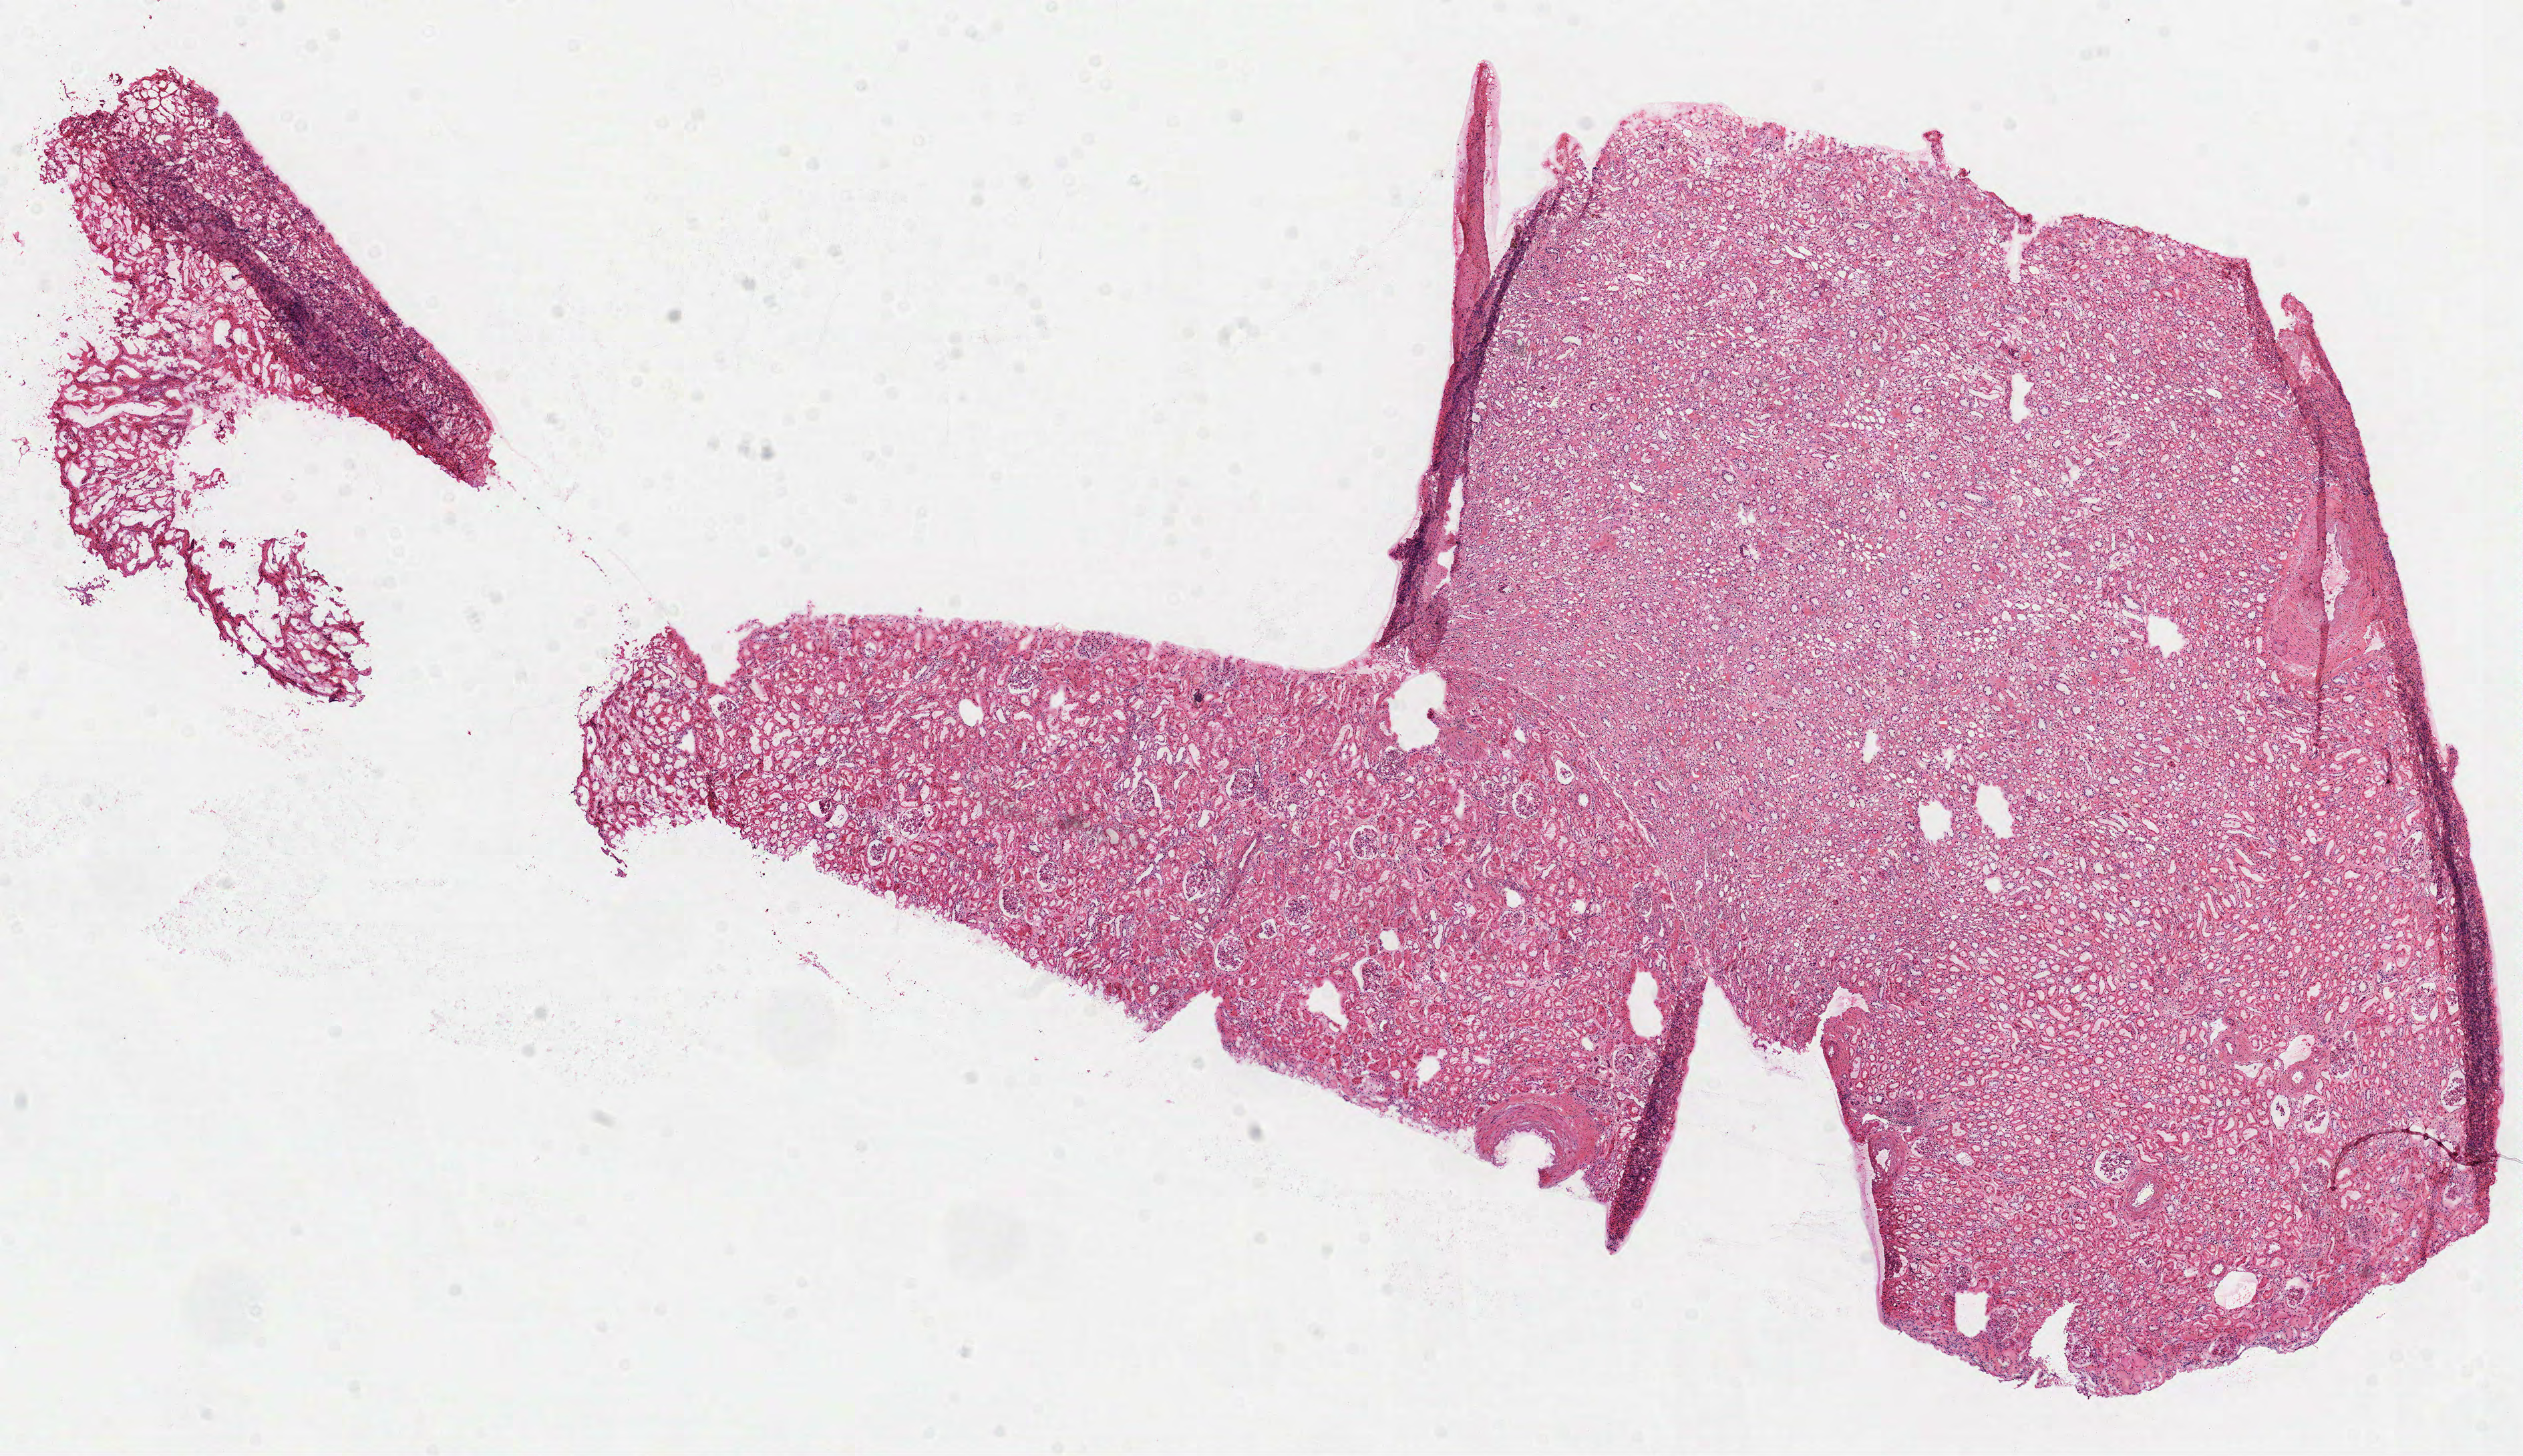
Whole-slide histology image, H&E-stained — low-resolution overview of the scanned area, about 15.2 x 8.8 mm (from a 40x scan), frozen section, sample: solid tissue normal (non-tumour tissue), kidney. Male patient; age at initial diagnosis 77 years.
This section: solid tissue normal sample (biorepository sample class). Patient diagnosis: Clear cell adenocarcinoma, NOS.